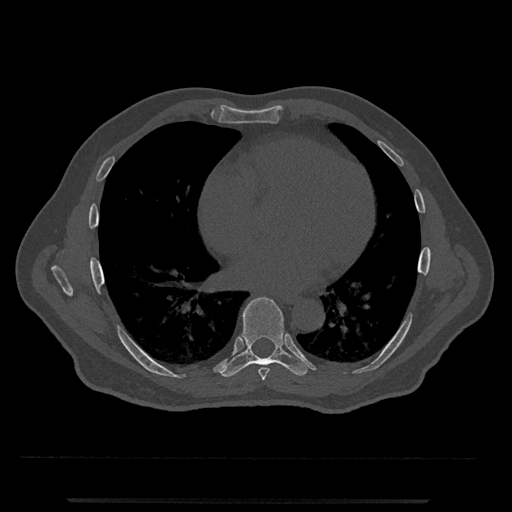
CT including the spine, one axial slice; position 644 of 797 along the scan axis; reconstruction kernel Br40s/3; bone window (W 1800 / L 400 HU); 512 × 512 image matrix. Male patient, age 63 years. Case-level facts recorded for this patient, not image findings: primary cancer: prostate.
Structures marked on this image (semi-automatically segmented with operator editing):
- T7 vertebra: box from (x=258, y=367) to (x=270, y=381) px
- T8 vertebra: (x=221, y=297)–(x=314, y=377)